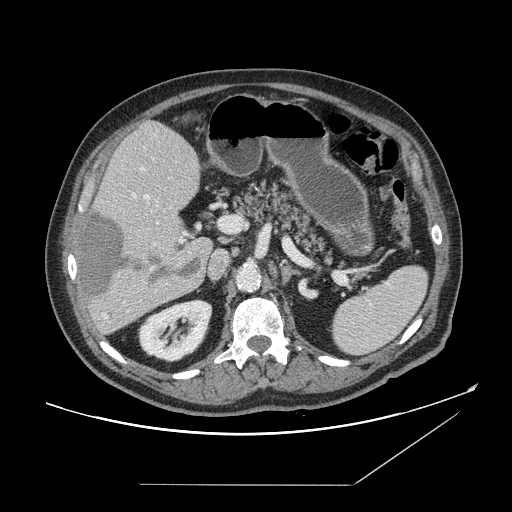
Contrast-enhanced abdominal CT, one axial slice; slice 89 of 166 in the series (ordered by position); intravenous contrast given; soft-tissue window (W 400 / L 40 HU); 512 × 512 image matrix. Male patient, age 80 years. Case-level facts recorded for this patient, not image findings: diagnosis: colorectal cancer liver metastases, imaged before liver resection; multiple liver metastases: no; largest metastasis: 2.2 cm; disease in both lobes: no.
Structures marked on this image (manually delineated by an expert):
- hepatic veins: bounding box <142,168,153,270> (left, top, right, bottom; pixels)
- liver: <79,122,212,335>
- planned liver remnant (the part of the liver to remain after resection): <98,122,212,248>
- portal vein (with intrahepatic branches): <133,195,231,243>
- liver metastasis: <85,213,204,300>